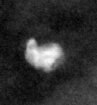
Region of interest cut from a scanned film mammogram (one marked finding), right breast, MLO view.
Marked abnormality: calcifications, morphology coarse / round and regular / lucent center; BI-RADS assessment category 2; subtlety rating 5 on a 1 (subtle) to 5 (obvious) scale; benign without callback (not worked up further).